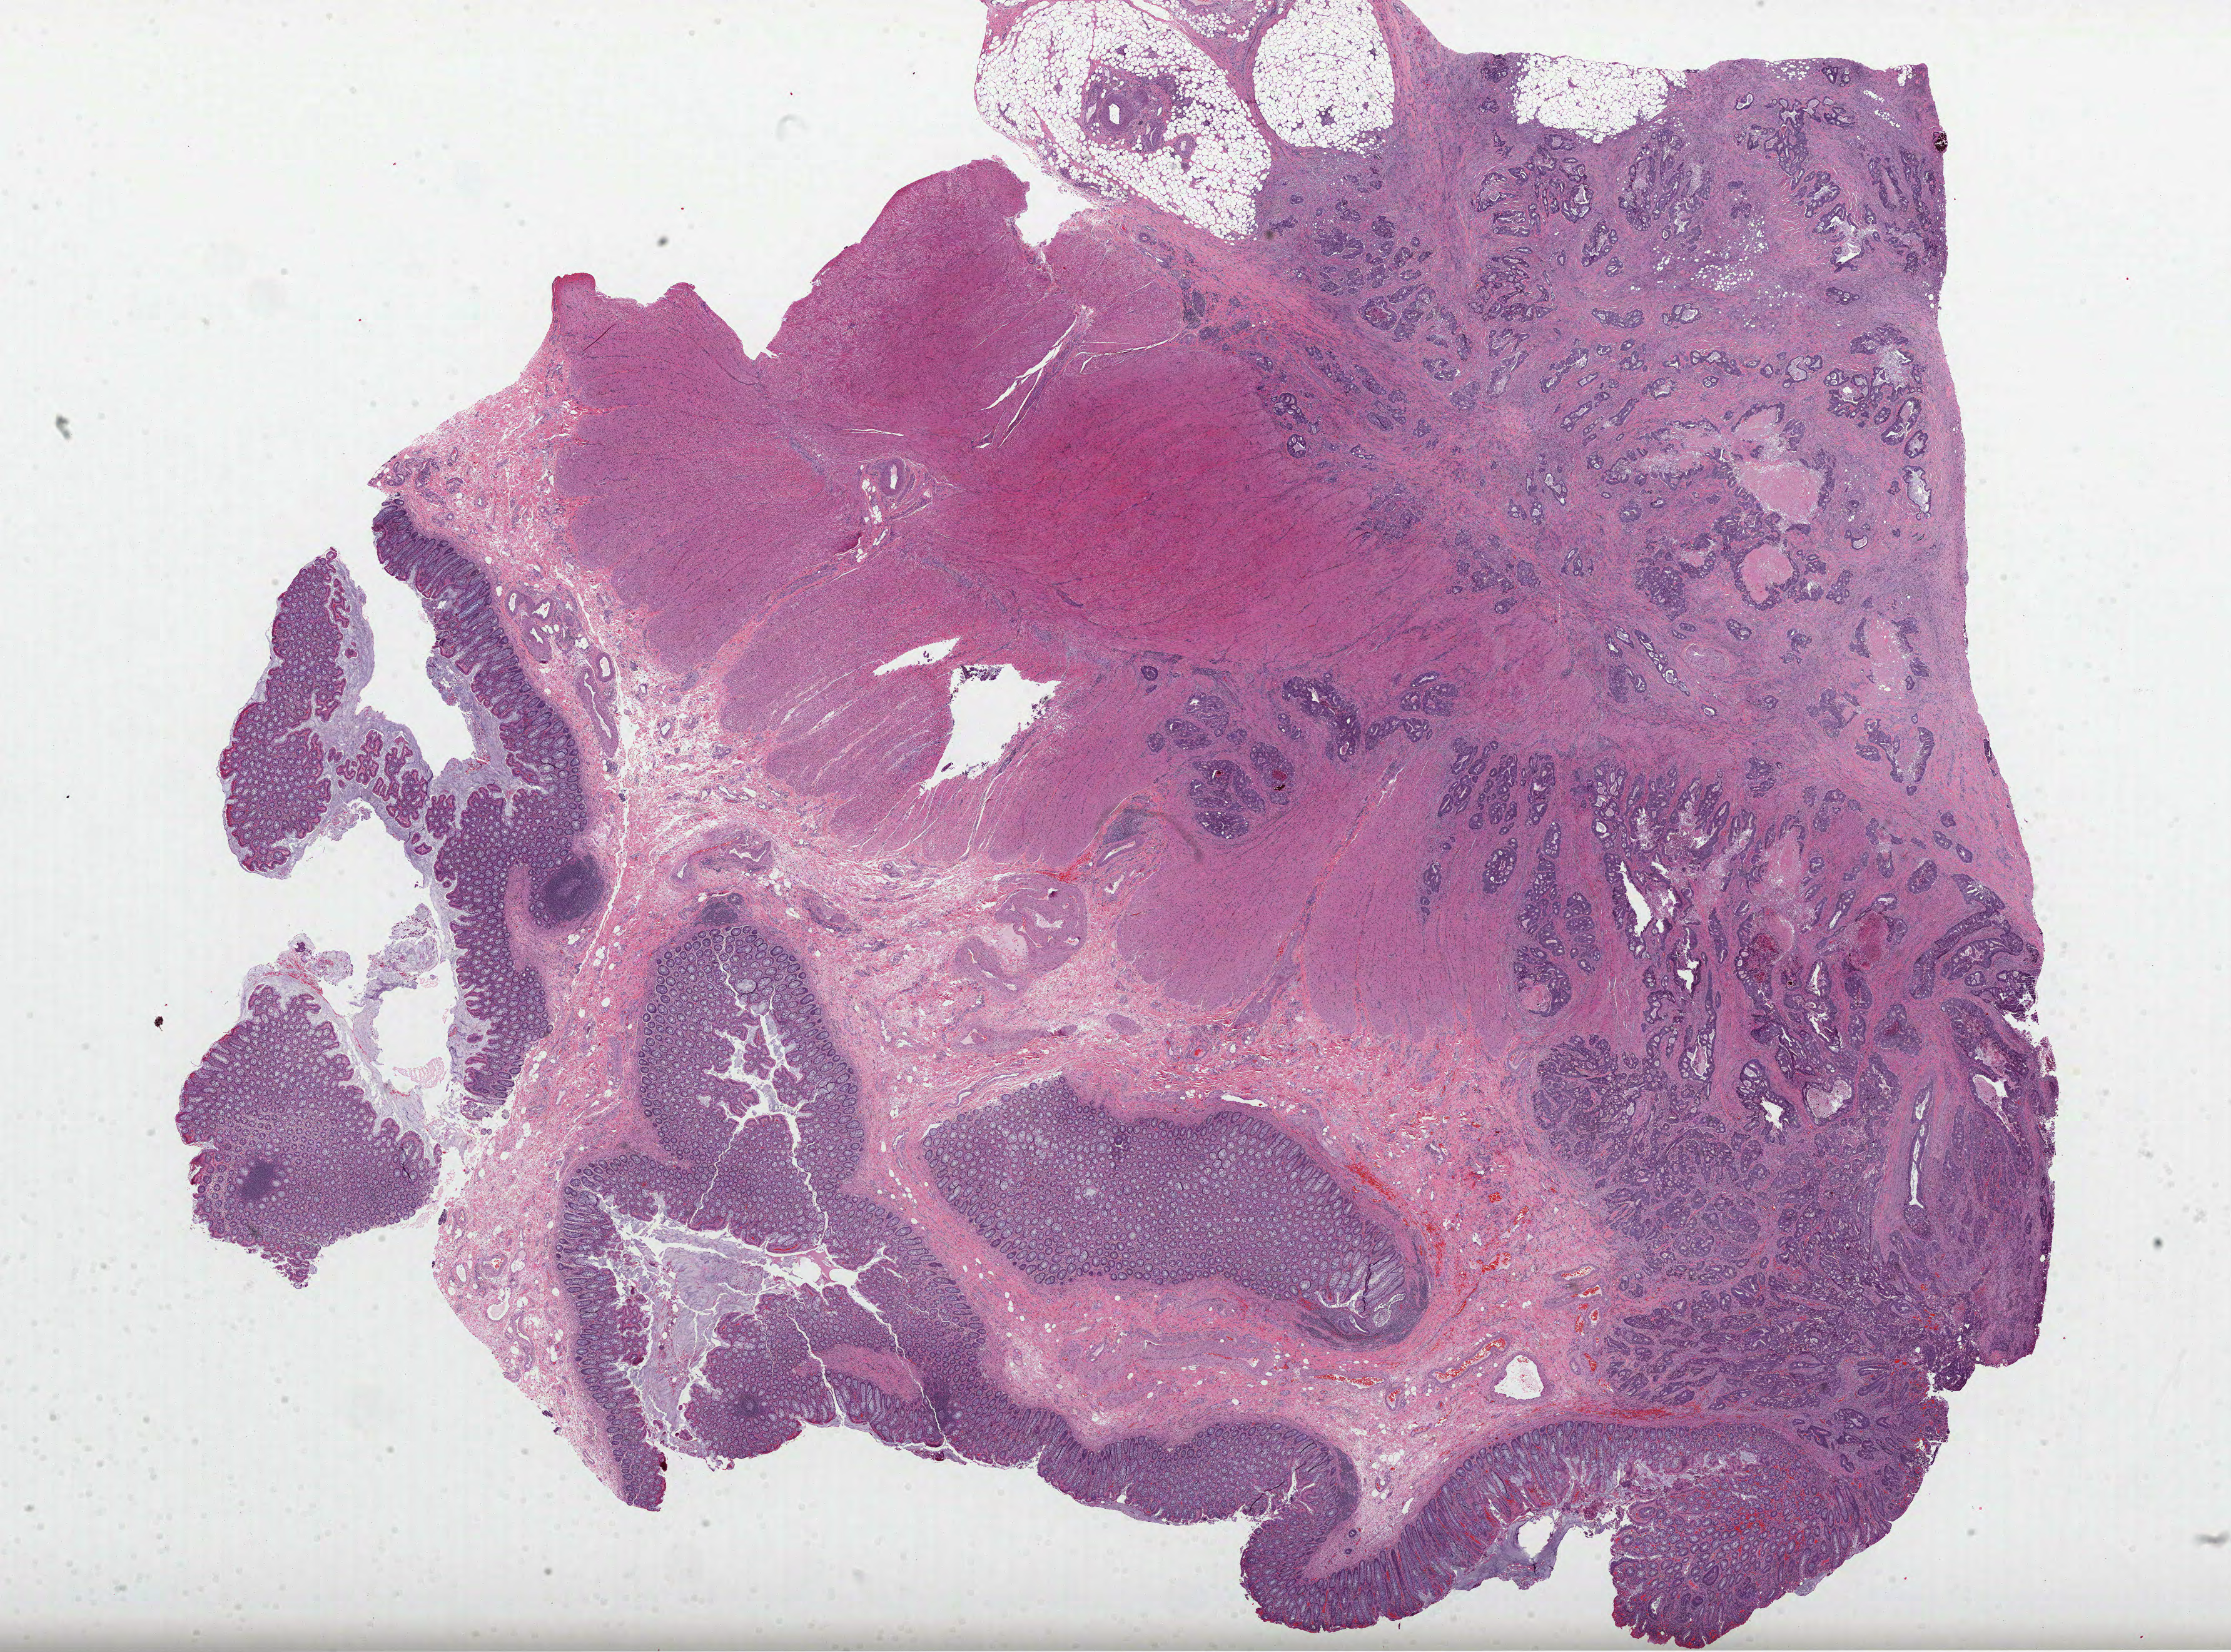
Whole-slide histology image, H&E-stained, a low-resolution overview of the entire scanned area, about 28.8 x 21.3 mm. Formalin-fixed paraffin-embedded (FFPE) diagnostic section. Rectum, primary tumour sample. Male patient; age at initial diagnosis 62 years.
• AJCC pathologic stage: IVA (7th edition)
• diagnosis: Adenocarcinoma, NOS (rectosigmoid junction)
• lymph nodes positive (case pathology): 7 of 22 examined